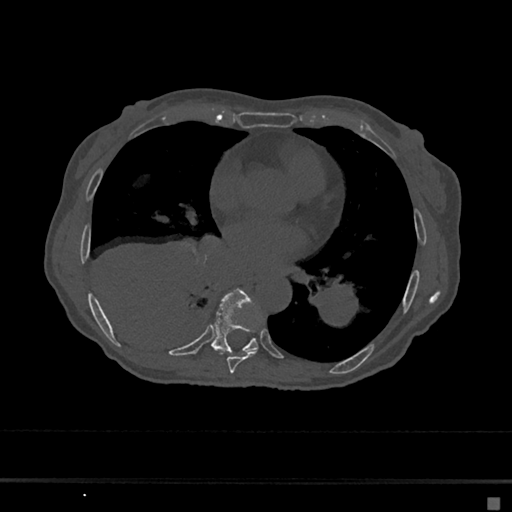
CT including the spine, one axial slice. Slice 347 of 797 in the series (ordered by position). Reconstruction kernel Br40s/3. 120 kVp. Bone window (W 1800 / L 400 HU). 0.5 mm slice thickness. 512 × 512 image matrix. Patient: female, 68 years. Case-level facts recorded for this patient, not image findings: primary cancer: renal.
Outlined on this slice (semi-automatic segmentation, software-assisted and operator-edited):
- T7 vertebra: bounding box [x1, y1, x2, y2] px = [220, 351, 257, 373]
- T8 vertebra: [211, 289, 259, 355]